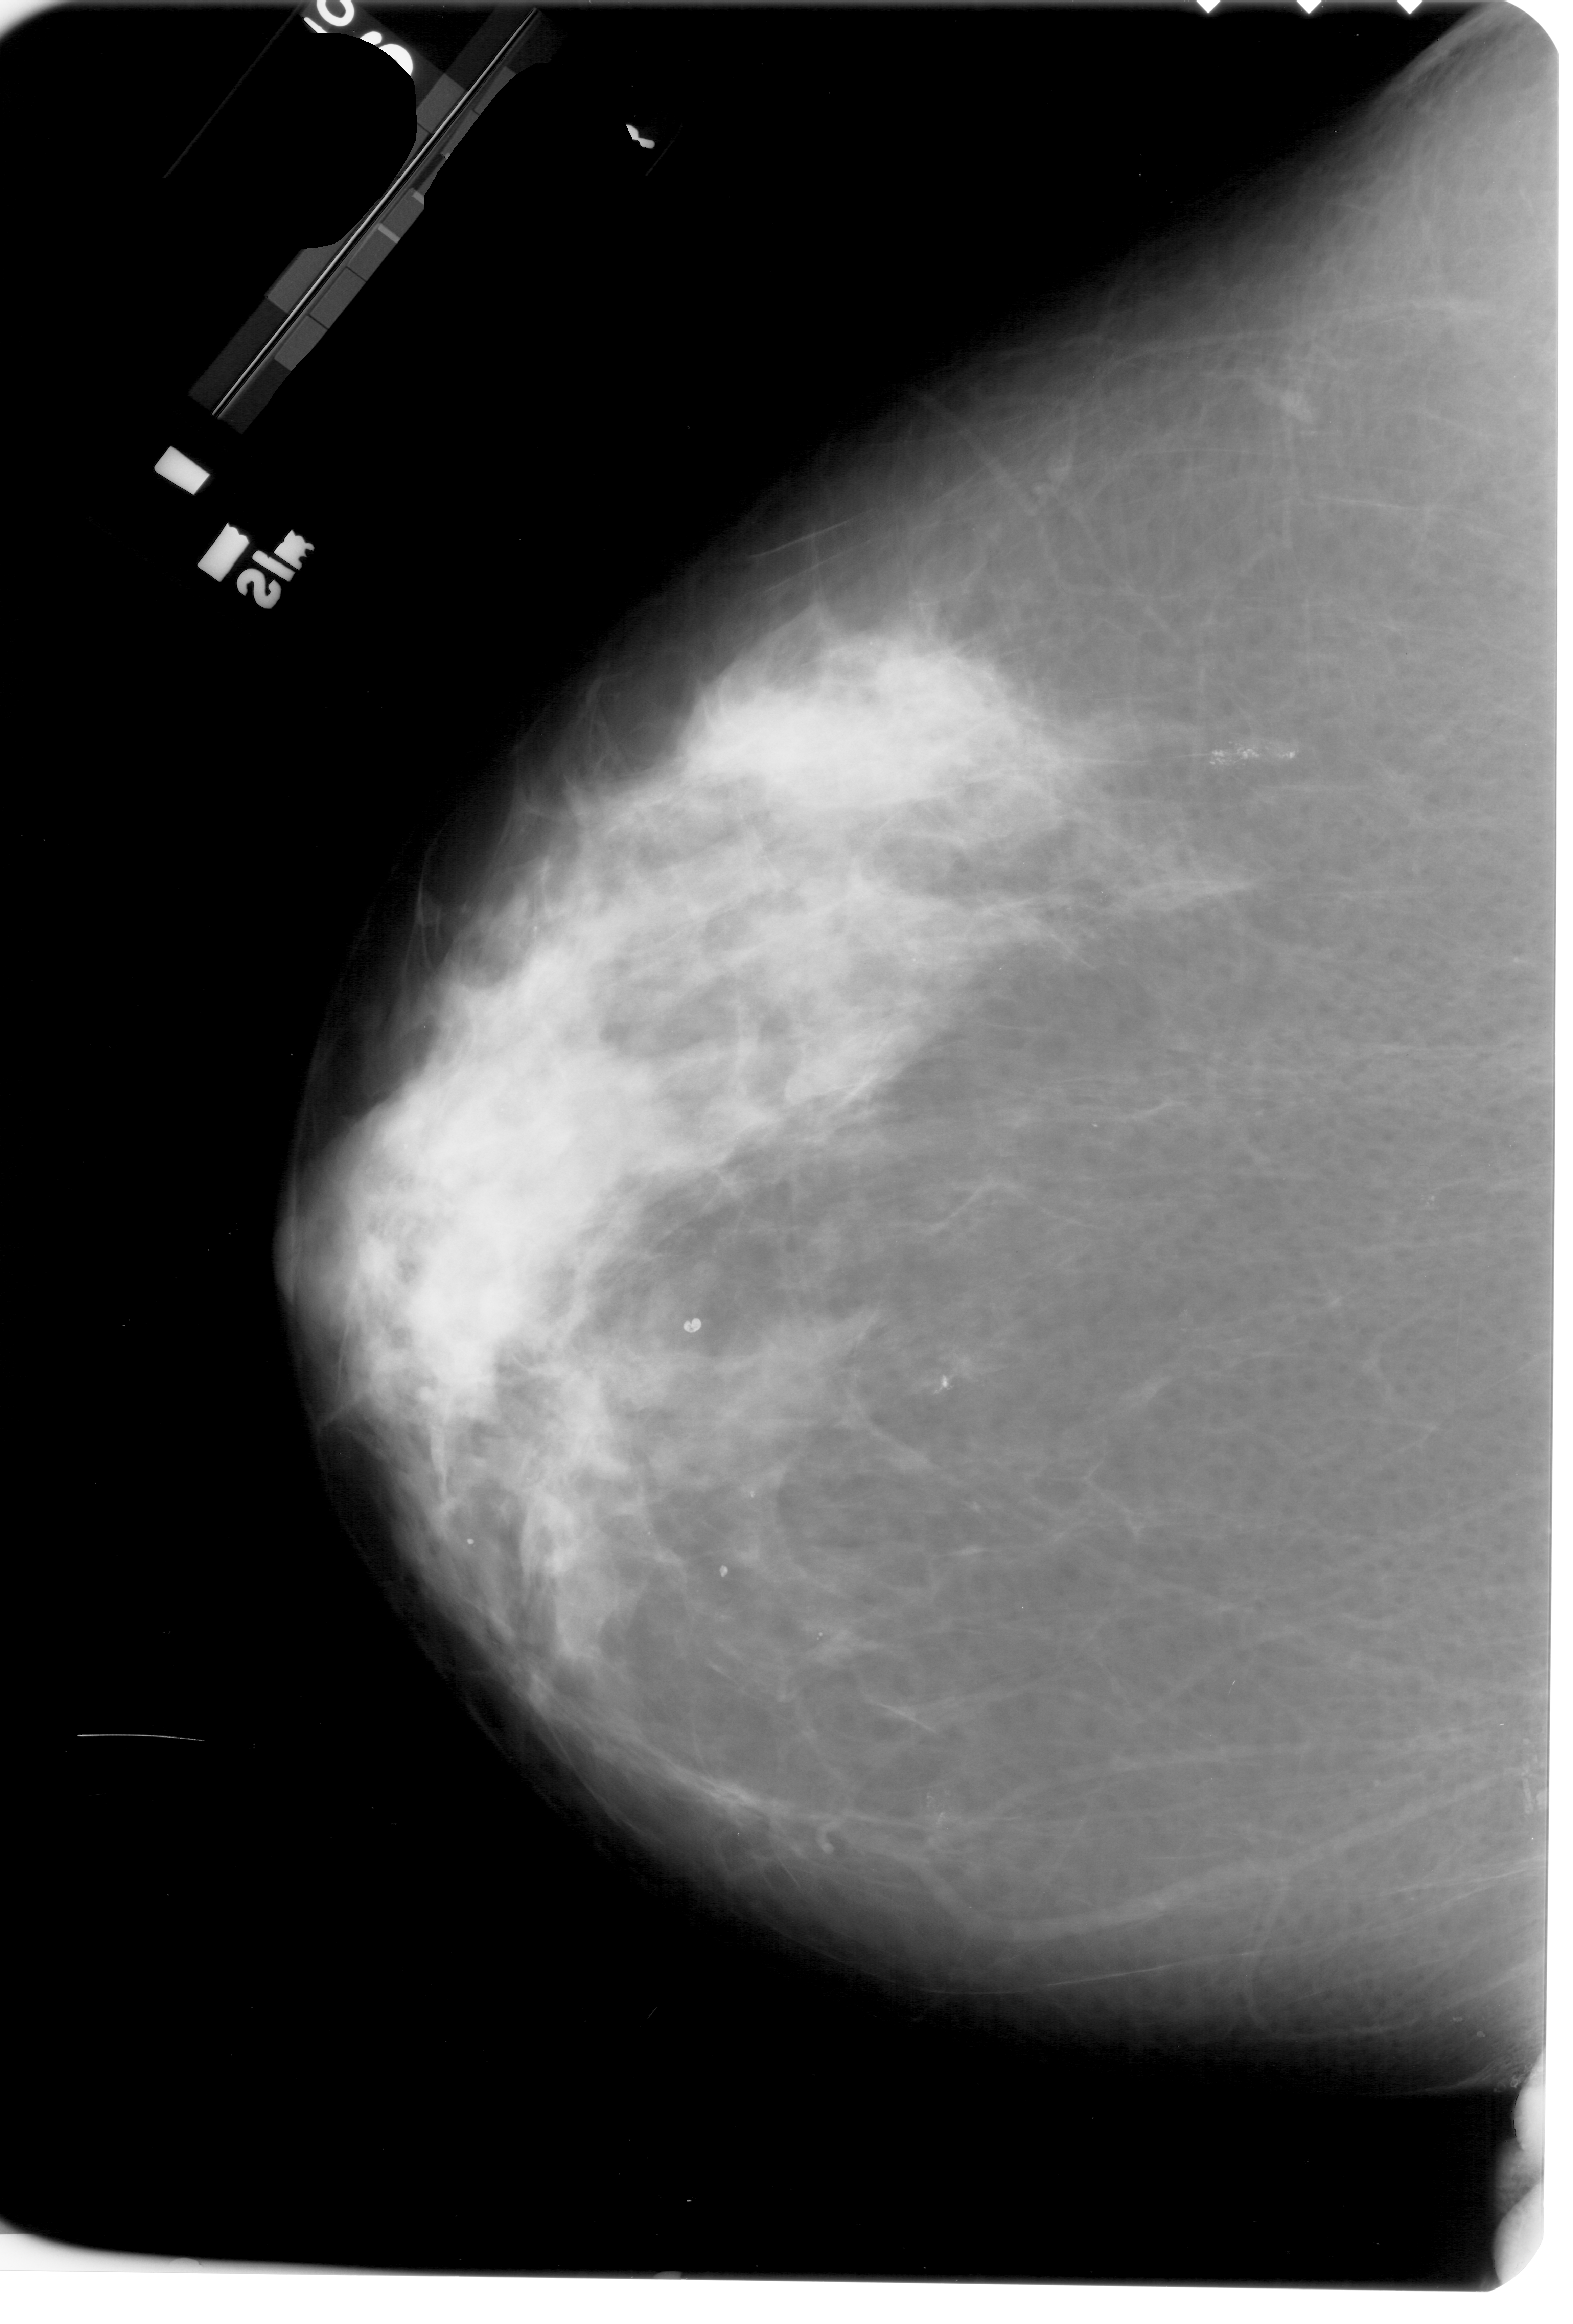
Mammogram (digitized film); left breast; CC view; BI-RADS breast density category 3 (scale 1–4).
- Finding: calcifications, morphology pleomorphic, distribution clustered; BI-RADS assessment category 4; pathology result (as recorded, not read from the image): benign.